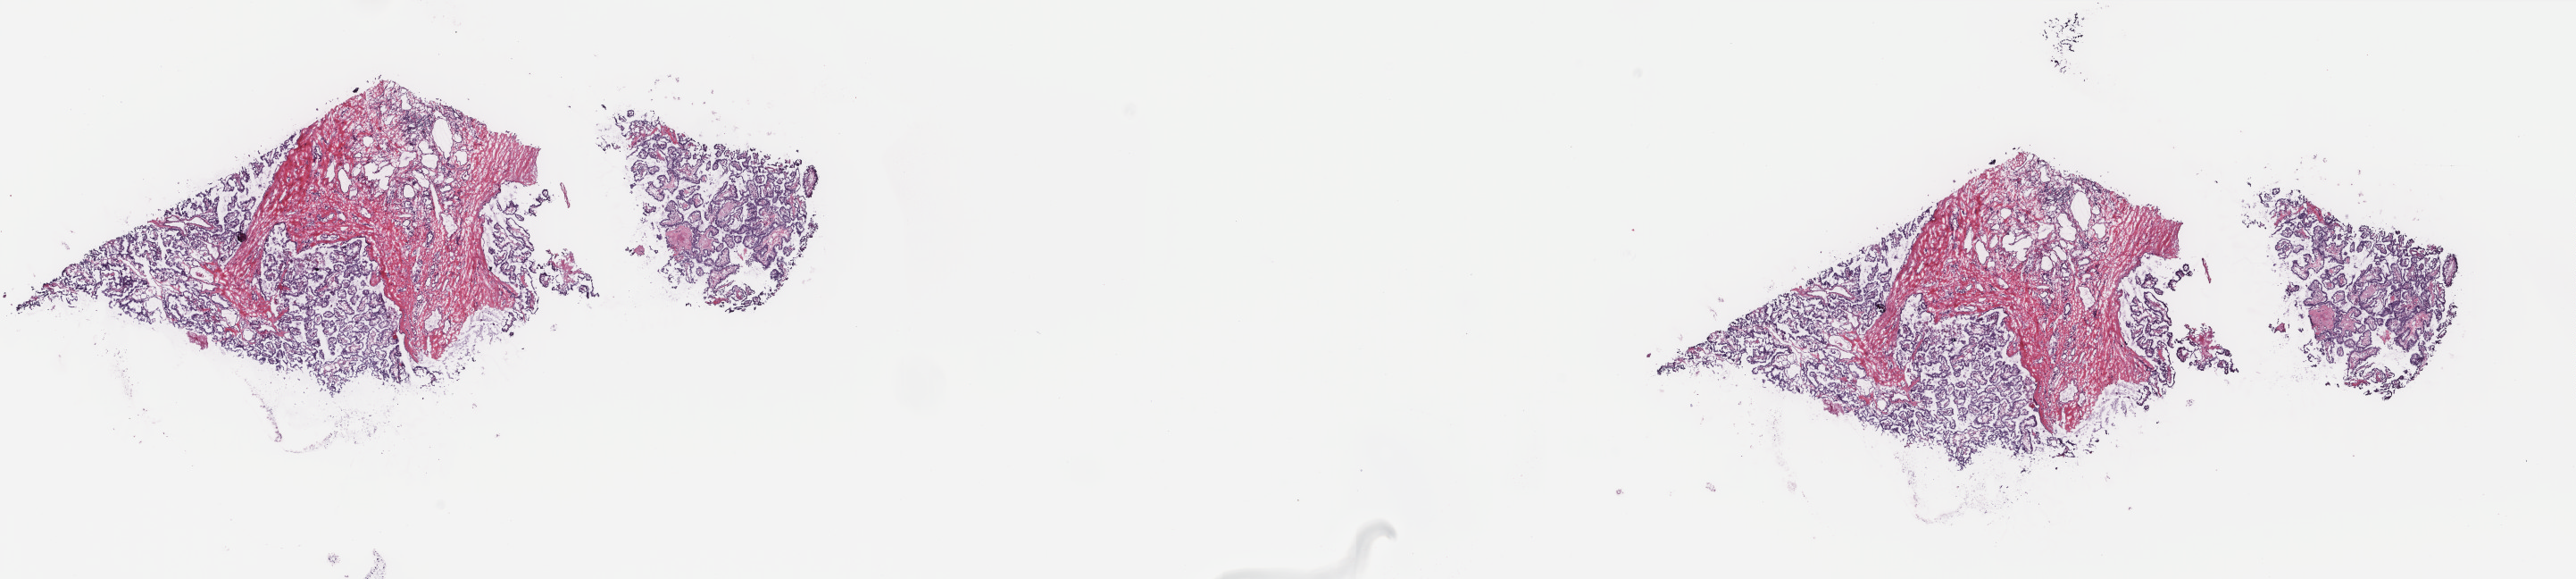
Whole-slide histology image, H&E — whole scanned area (about 22.9 x 5.1 mm, acquisition: 40x scan) shown as a low-resolution overview. Frozen section. Sample: primary tumour, thyroid. Female, age 28 years at initial diagnosis. Slide review estimates, as recorded: tumour cells 70%, tumour nuclei 90%, normal cells 0%, stromal cells 25%, necrosis 5%. Infiltration values recorded for this section: lymphocyte infiltration 1%, monocyte infiltration 1%, neutrophil infiltration 0%.
Lymph nodes positive (case pathology): 2 of 14 examined. Pathologic diagnosis: Papillary adenocarcinoma, NOS (thyroid gland). AJCC pathologic stage: I (6th edition).